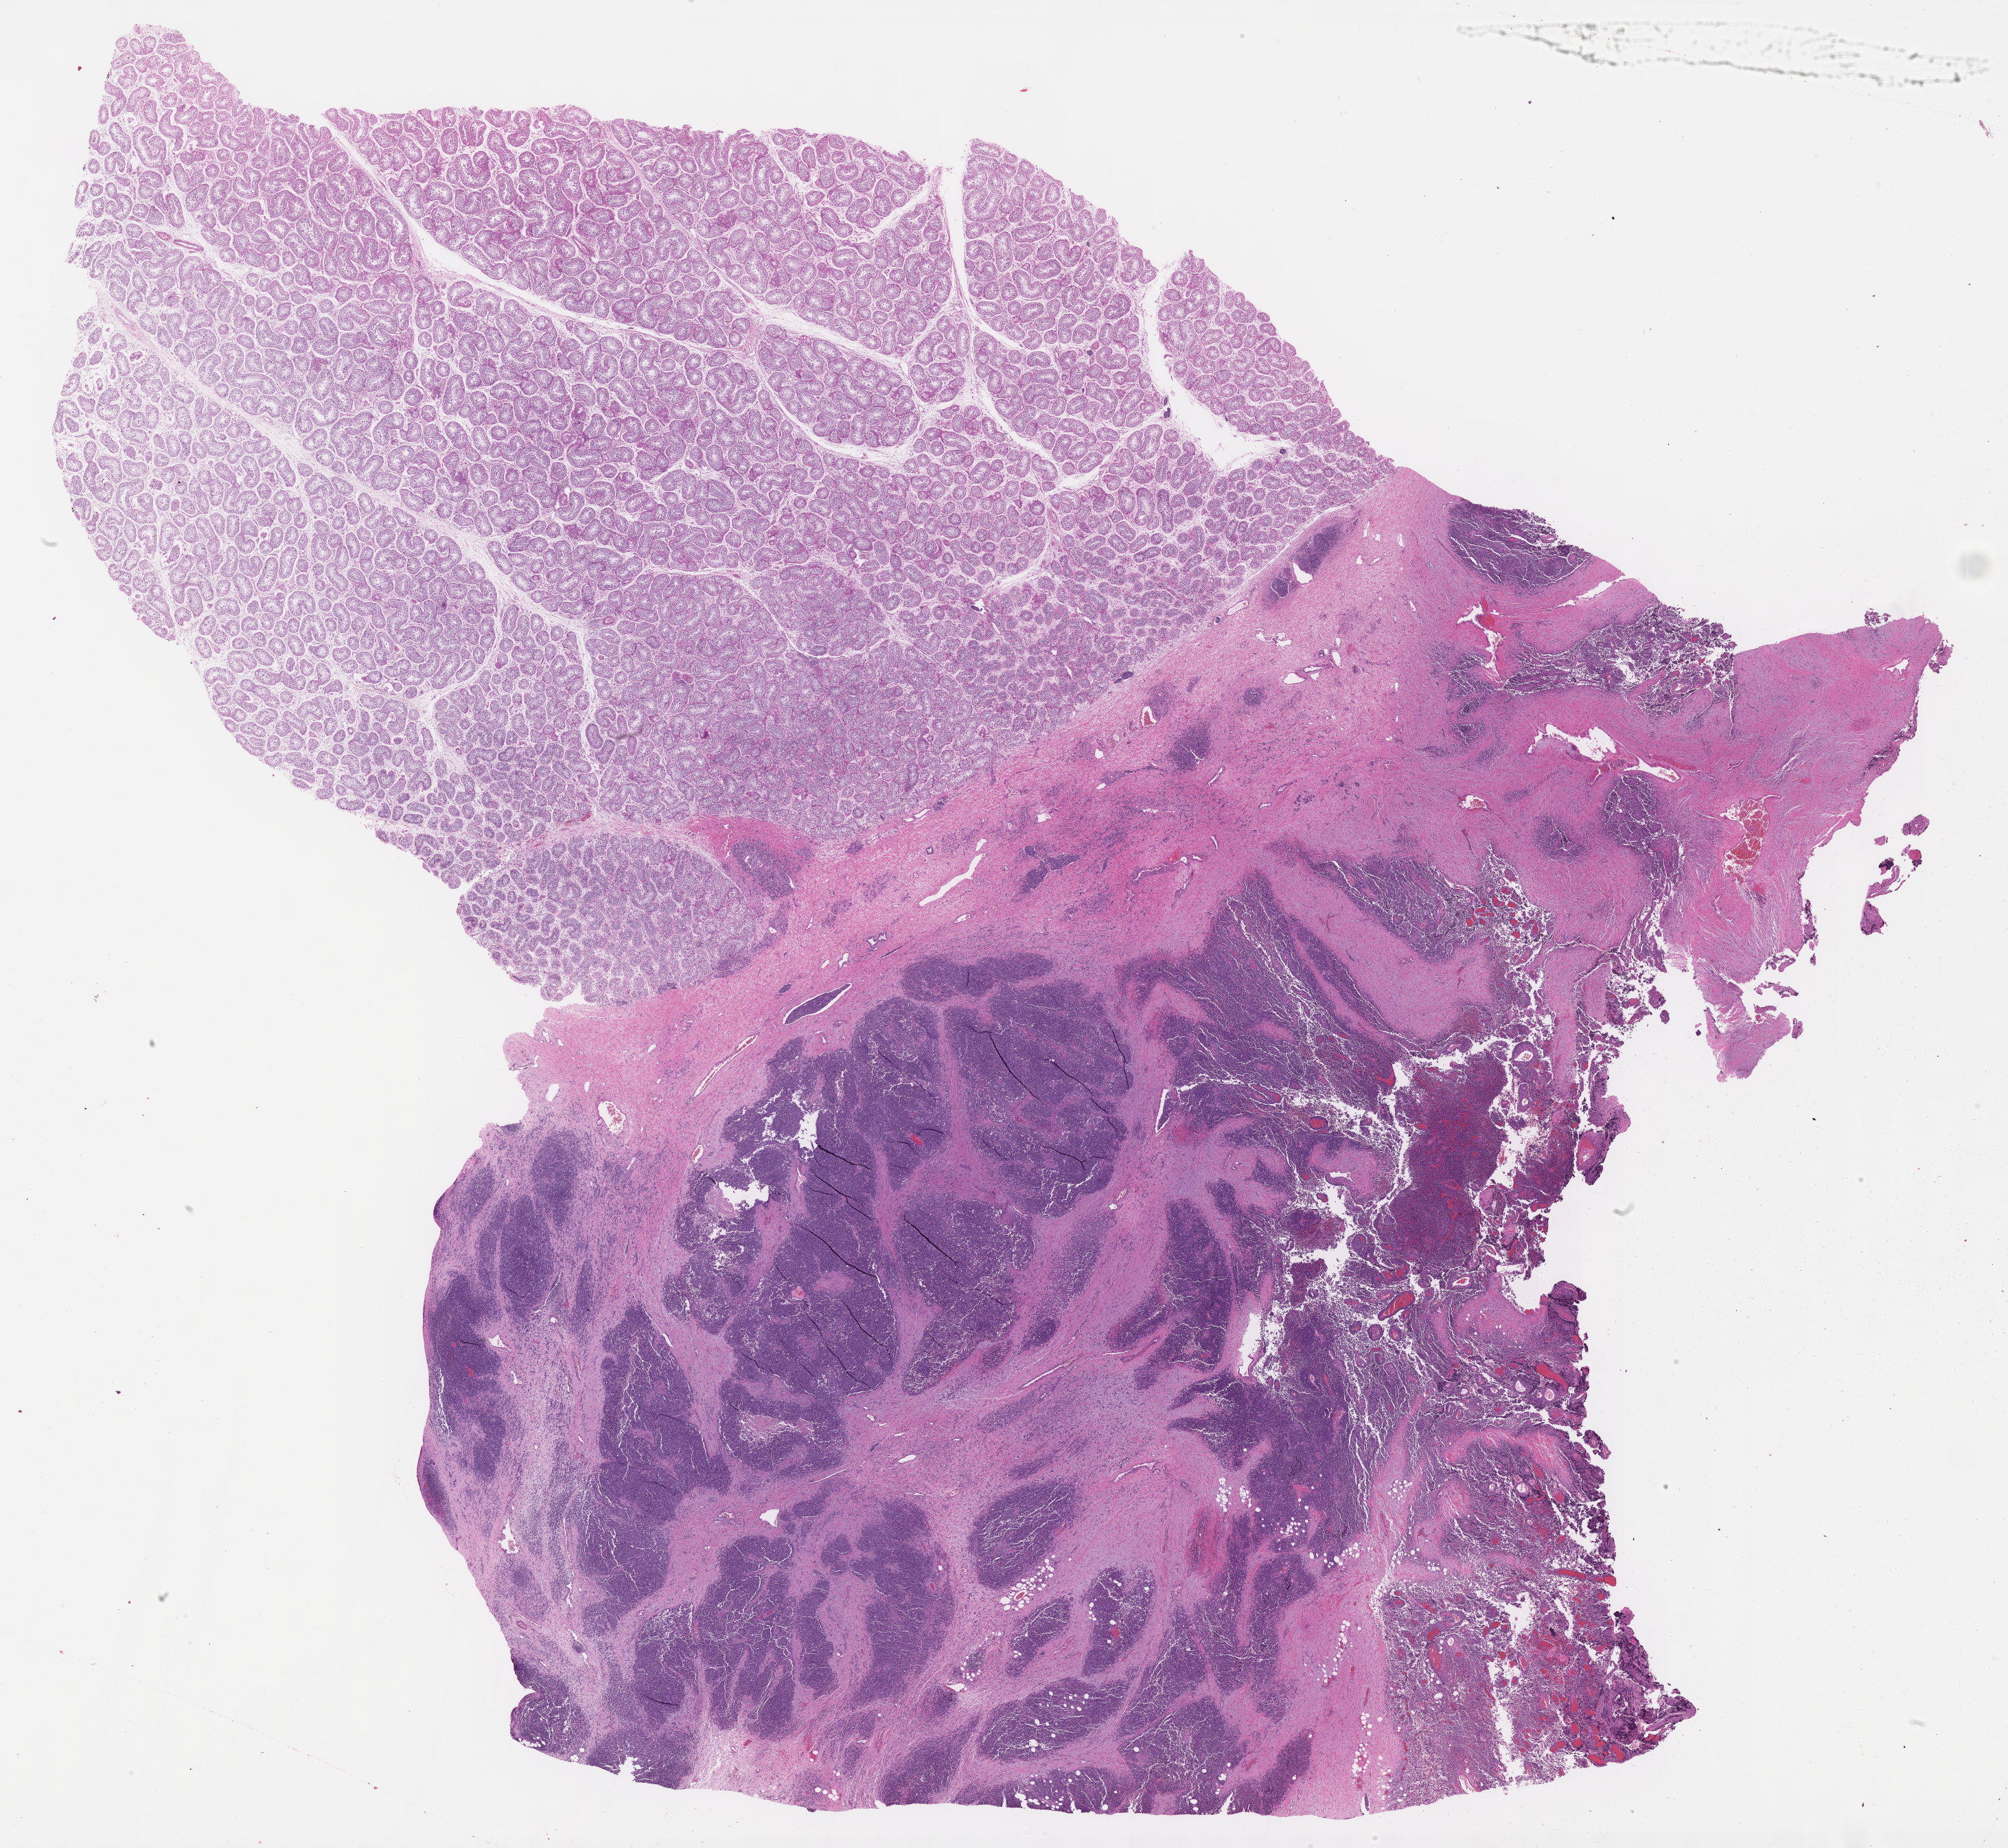
H&E whole-slide image of tumor tissue — whole scanned area (about 23.6 x 21.8 mm) shown as a low-resolution overview, FFPE section, site: paratesticular, right. Patient: male, age 15.1 years at diagnosis.
Diagnosis: rhabdomyosarcoma; histological classification: embryonal rhabdomyosarcoma. Primary site (case record): testis-paratesticular. Stage (as recorded): 1. Metastatic status at presentation (as recorded): non-metastatic (confirmed).